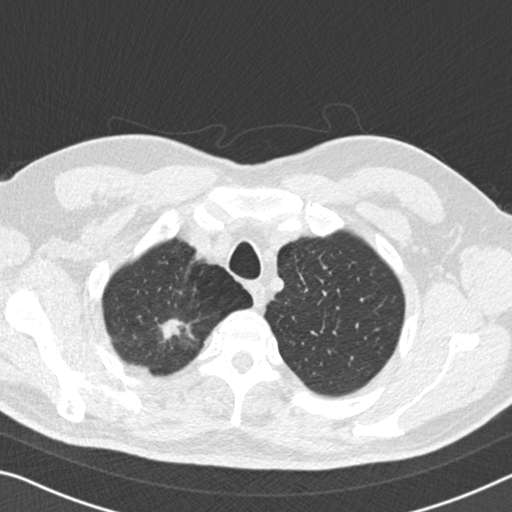
Chest CT (low-dose screening protocol), one axial image; third screening round (two years after baseline); lung window (W 1500 / L -600 HU); 2 mm slice thickness; standard (soft-tissue) reconstruction kernel (B30f); slice 24 of 167 in the series. Male, age 56 years at enrolment.
Expert reader's lesion annotation, bounding box (x1, y1, x2, y2) in pixels: (143, 306, 204, 358). The exam's reader record, not a measurement of the box and not confirmed to be the same lesion: non-calcified nodule or mass ≥4 mm, right upper lobe, 13 × 13 mm, spiculated (stellate) margins, soft tissue attenuation, pre-existing on the prior screen: yes; interval growth: yes. Participant outcome: lung cancer diagnosed 97 days after this screen — adenocarcinoma, NOS, right upper lobe, moderately differentiated (G2), stage IA (AJCC 6th edition), 9 mm at pathology.